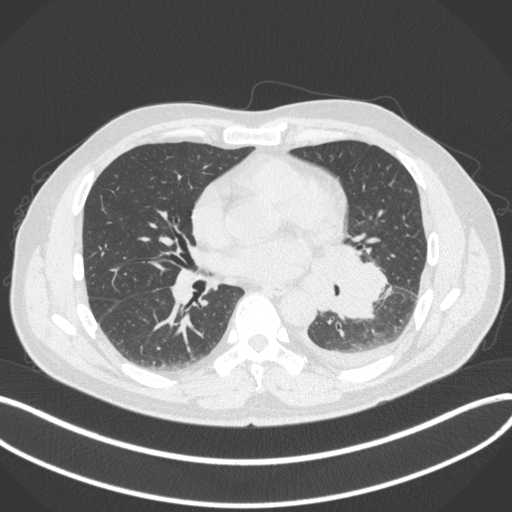
Chest CT, one axial slice; slice 174 of 350 in the series (ordered by position); reconstruction kernel B31f; 120 kVp; lung window (W 1500 / L -600 HU); 1 mm slice thickness; 512 × 512 image matrix, field of view 400 × 400 mm. Patient: male, 58 years. From the clinical record (not read from this slice): clinical TNM (as recorded): T3 N1 M1b; histopathological grade: G3.
Annotated regions visible in this slice (rectangle marked by the reading radiologist):
- lung tumour (recorded histology: small cell carcinoma): bounding box [x1, y1, x2, y2] px = [312, 234, 393, 328]